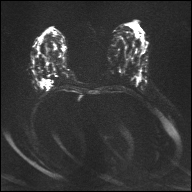
Breast MRI, one axial slice; slice 18 of 32 in the series (ordered by position); diffusion-weighted series; image 2 of 4 stored at this slice position (different b-values; order by instance number); 1.5 T; 192 × 192 image matrix. Female patient.
Structures marked on this image (expert manual segmentation):
- tumour on diffusion-weighted imaging: bounding box [x1, y1, x2, y2] px = [40, 78, 50, 86]